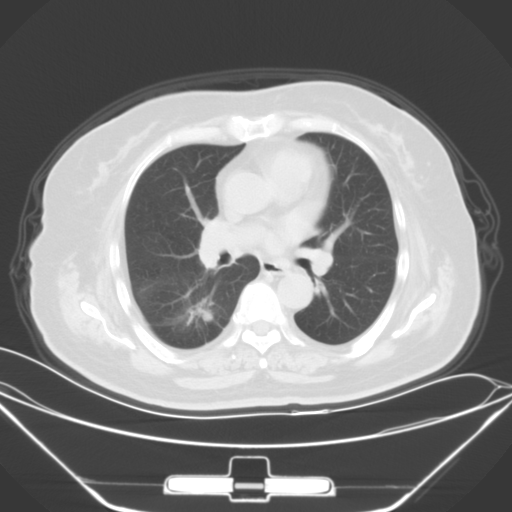
Chest CT, one axial slice. Slice 35 of 64 in the series (ordered by position). Lung window (W 1500 / L -600 HU). 5 mm slice thickness. 512 × 512 image matrix, field of view 396 × 396 mm. Female patient, age 70 years. From the clinical record (not read from this slice): clinical TNM (as recorded): T2 N0 M3.
Outlined on this slice (rectangle marked by the reading radiologist):
- lung tumour (recorded histology: adenocarcinoma): bounding box <155,291,226,339> (left, top, right, bottom; pixels)